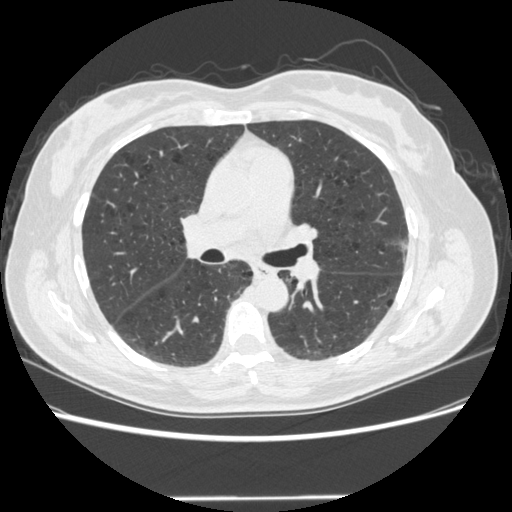
Low-dose screening chest CT, axial slice, baseline screening round, lung window (W 1500 / L -600 HU), standard (soft-tissue) reconstruction kernel (STANDARD), slice 183 of 301 in the series. Female, age 61 years at enrolment.
Expert-annotated lung lesion, bounding box (x1, y1, x2, y2) in pixels: (383, 227, 429, 278). Screening reader's record for this exam: no non-calcified nodule ≥4 mm recorded.